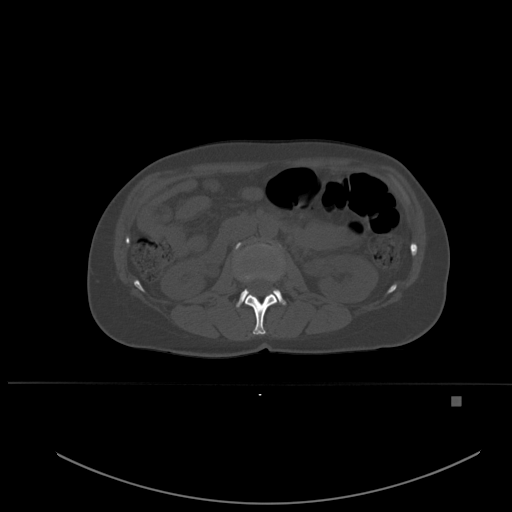
CT including the spine, one axial slice; slice 224 of 651 in the series (ordered by position); bone window (W 1800 / L 400 HU); 512 × 512 image matrix, field of view 443 × 443 mm. Patient: female, 49 years. Case-level facts recorded for this patient, not image findings: primary cancer: breast; vertebrae with lytic lesions (as recorded): L3, T12, L4.
Structures marked on this image (semi-automatic segmentation, software-assisted and operator-edited):
- L1 vertebra: bounding box <245,294,277,335> (left, top, right, bottom; pixels)
- L2 vertebra: <236,243,286,307>